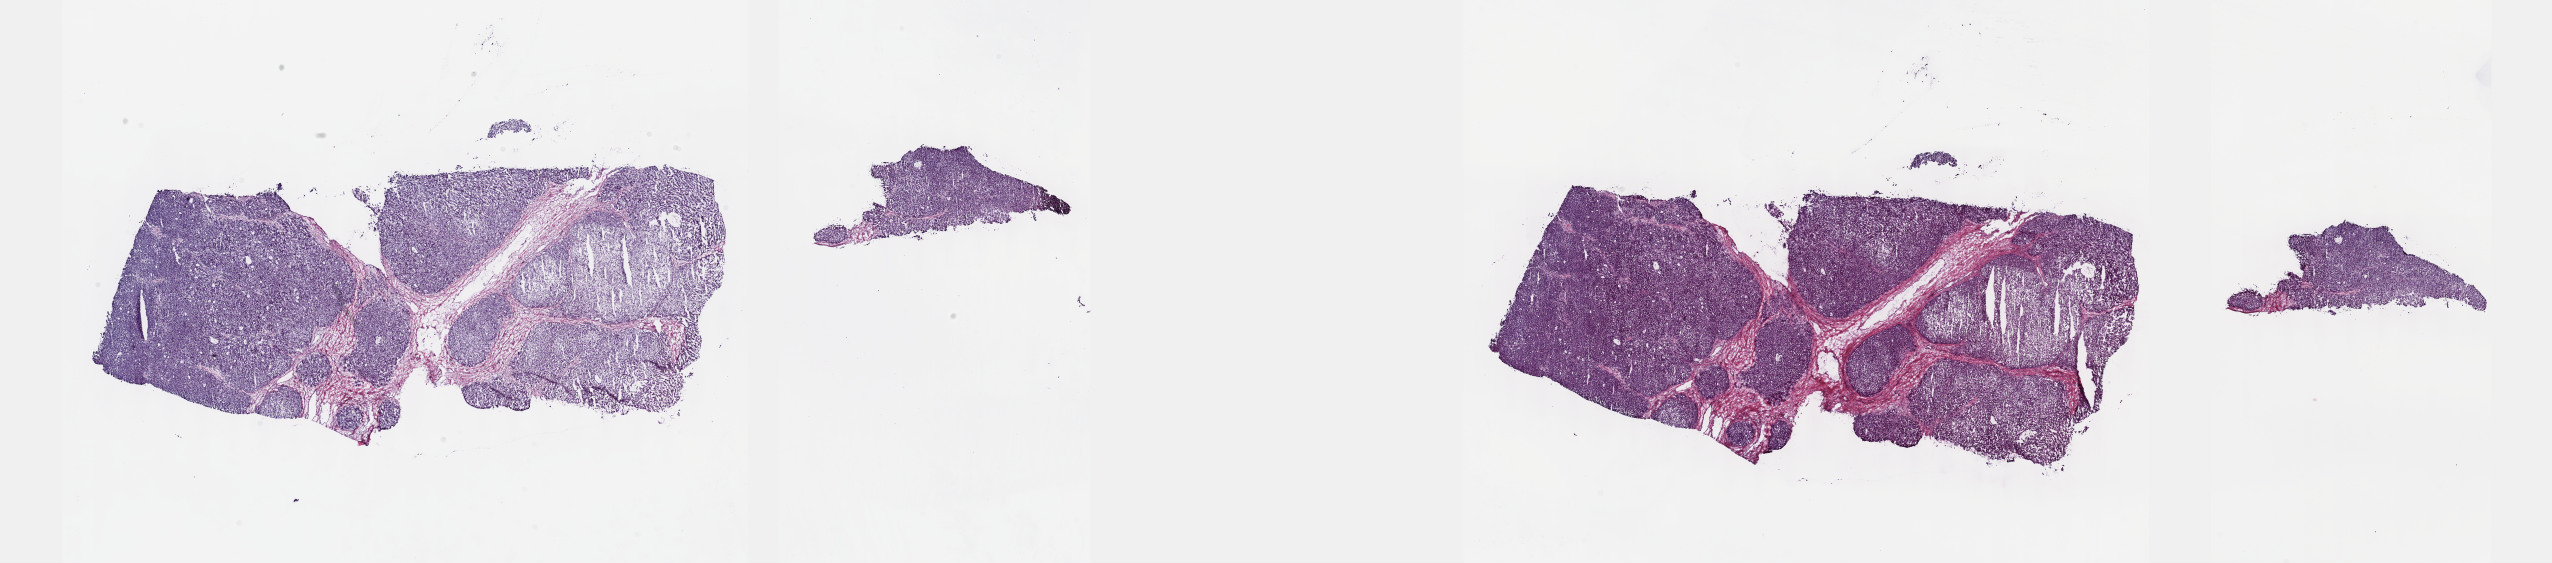
Digitized H&E tissue section (whole slide), a low-resolution overview of the entire scanned area, about 41.2 x 9.1 mm; frozen section; liver, primary tumour sample. Male patient; age at initial diagnosis 16 years. Histologic grade: G1 (well differentiated). Pathologist review of this section (percent, as recorded): tumour cells 80%, tumour nuclei 80%, normal cells 0%, stromal cells 20%, necrosis 0%. Inflammatory infiltration, as recorded: lymphocyte infiltration 3%, monocyte infiltration 1%, neutrophil infiltration 1%.
* TNM: T3 N0 MX
* AJCC pathologic stage: IIIA (7th edition)
* pathologic diagnosis: Hepatocellular carcinoma, NOS